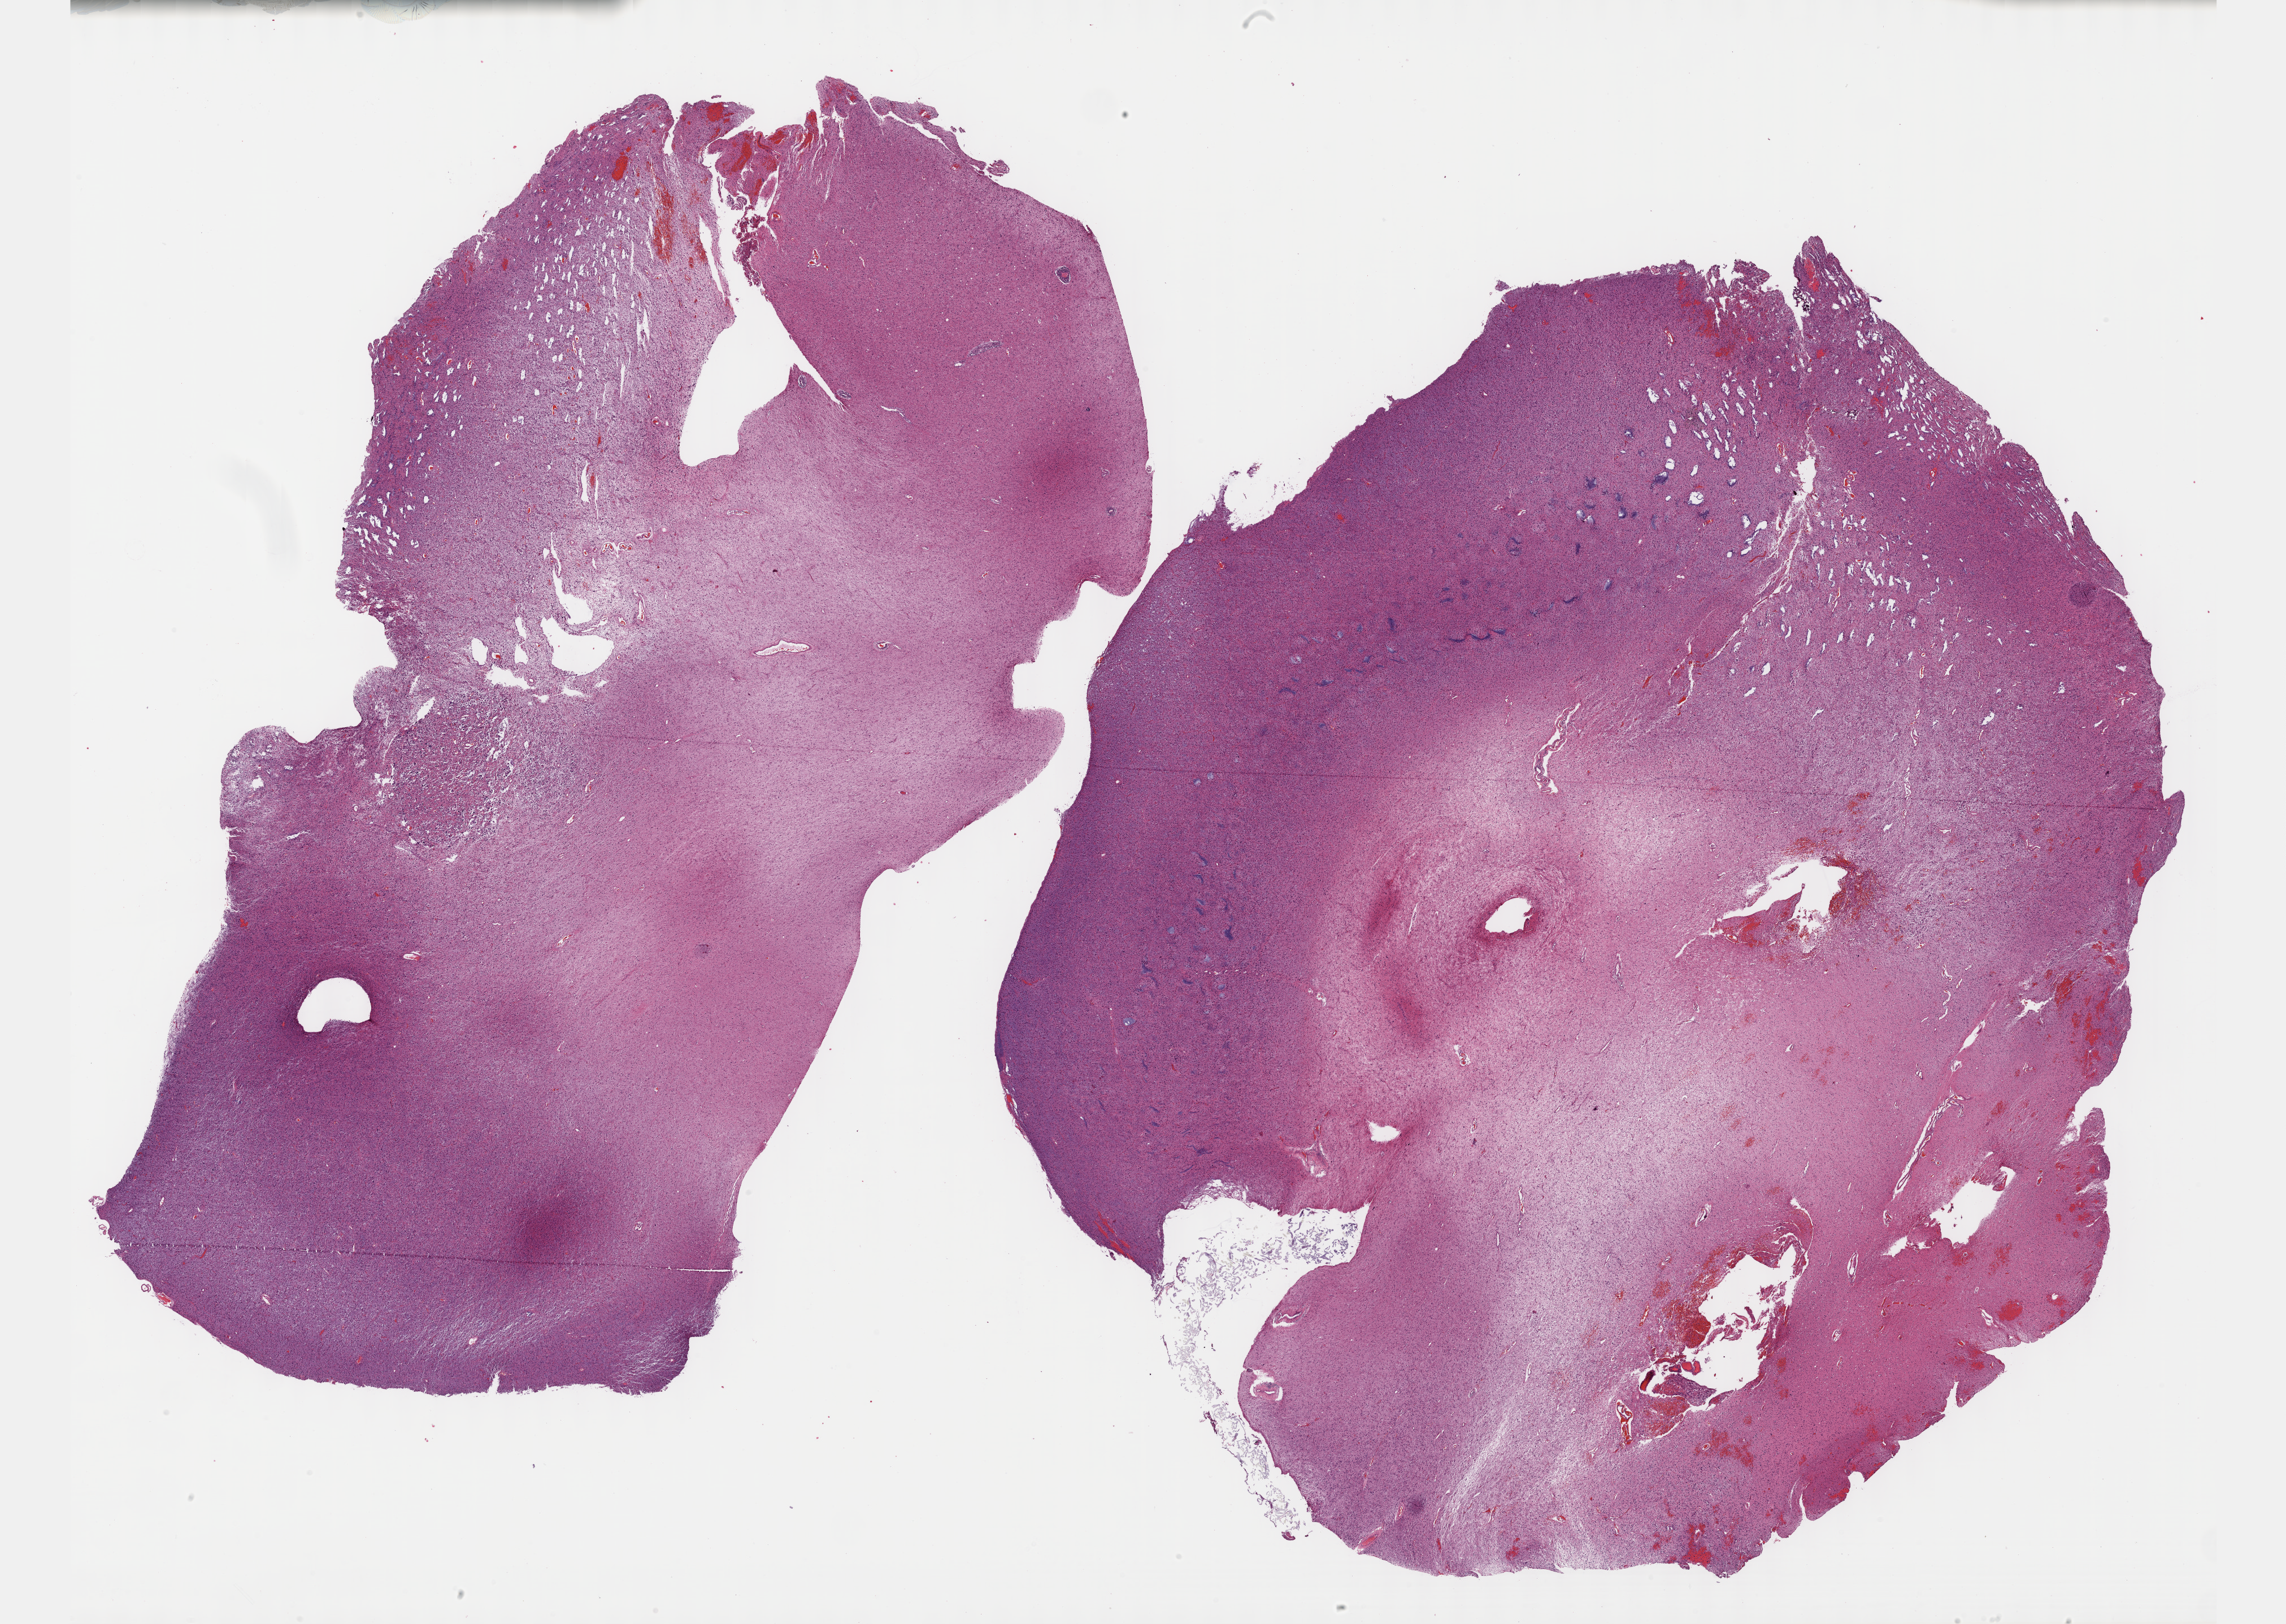
Digitized H&E-stained tissue section (whole slide) — shown as a low-resolution overview of the whole scanned area (about 32.7 x 23.2 mm, from a 40x scan), formalin-fixed paraffin-embedded (FFPE) diagnostic section, brain, primary tumour sample. Male patient; age at initial diagnosis 28 years. Histologic grade: G2 (moderately differentiated).
Histologic diagnosis: Astrocytoma, NOS (cerebrum). Laterality: right.